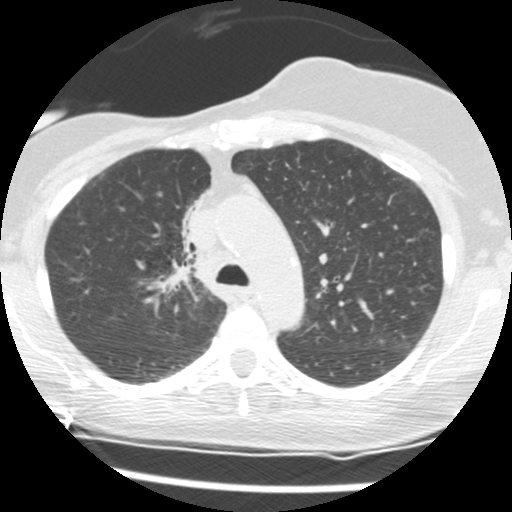
Chest CT (low-dose screening protocol), one axial image, second screening round (one year after baseline), lung window (W 1500 / L -600 HU), slice 41 of 165 in the series. Female participant, aged 56 years at enrolment.
Expert-annotated lung lesion, bounding box <154,192,212,273> (left, top, right, bottom; pixels). The screening reader recorded 2 non-calcified nodules or masses ≥4 mm on this exam (right middle lobe, right lower lobe); which of them this box marks is not recorded. Official screen result: positive, change unspecified: nodule(s) >= 4 mm or enlarging nodule(s), mass(es), or other non-specific abnormalities suspicious for lung cancer.